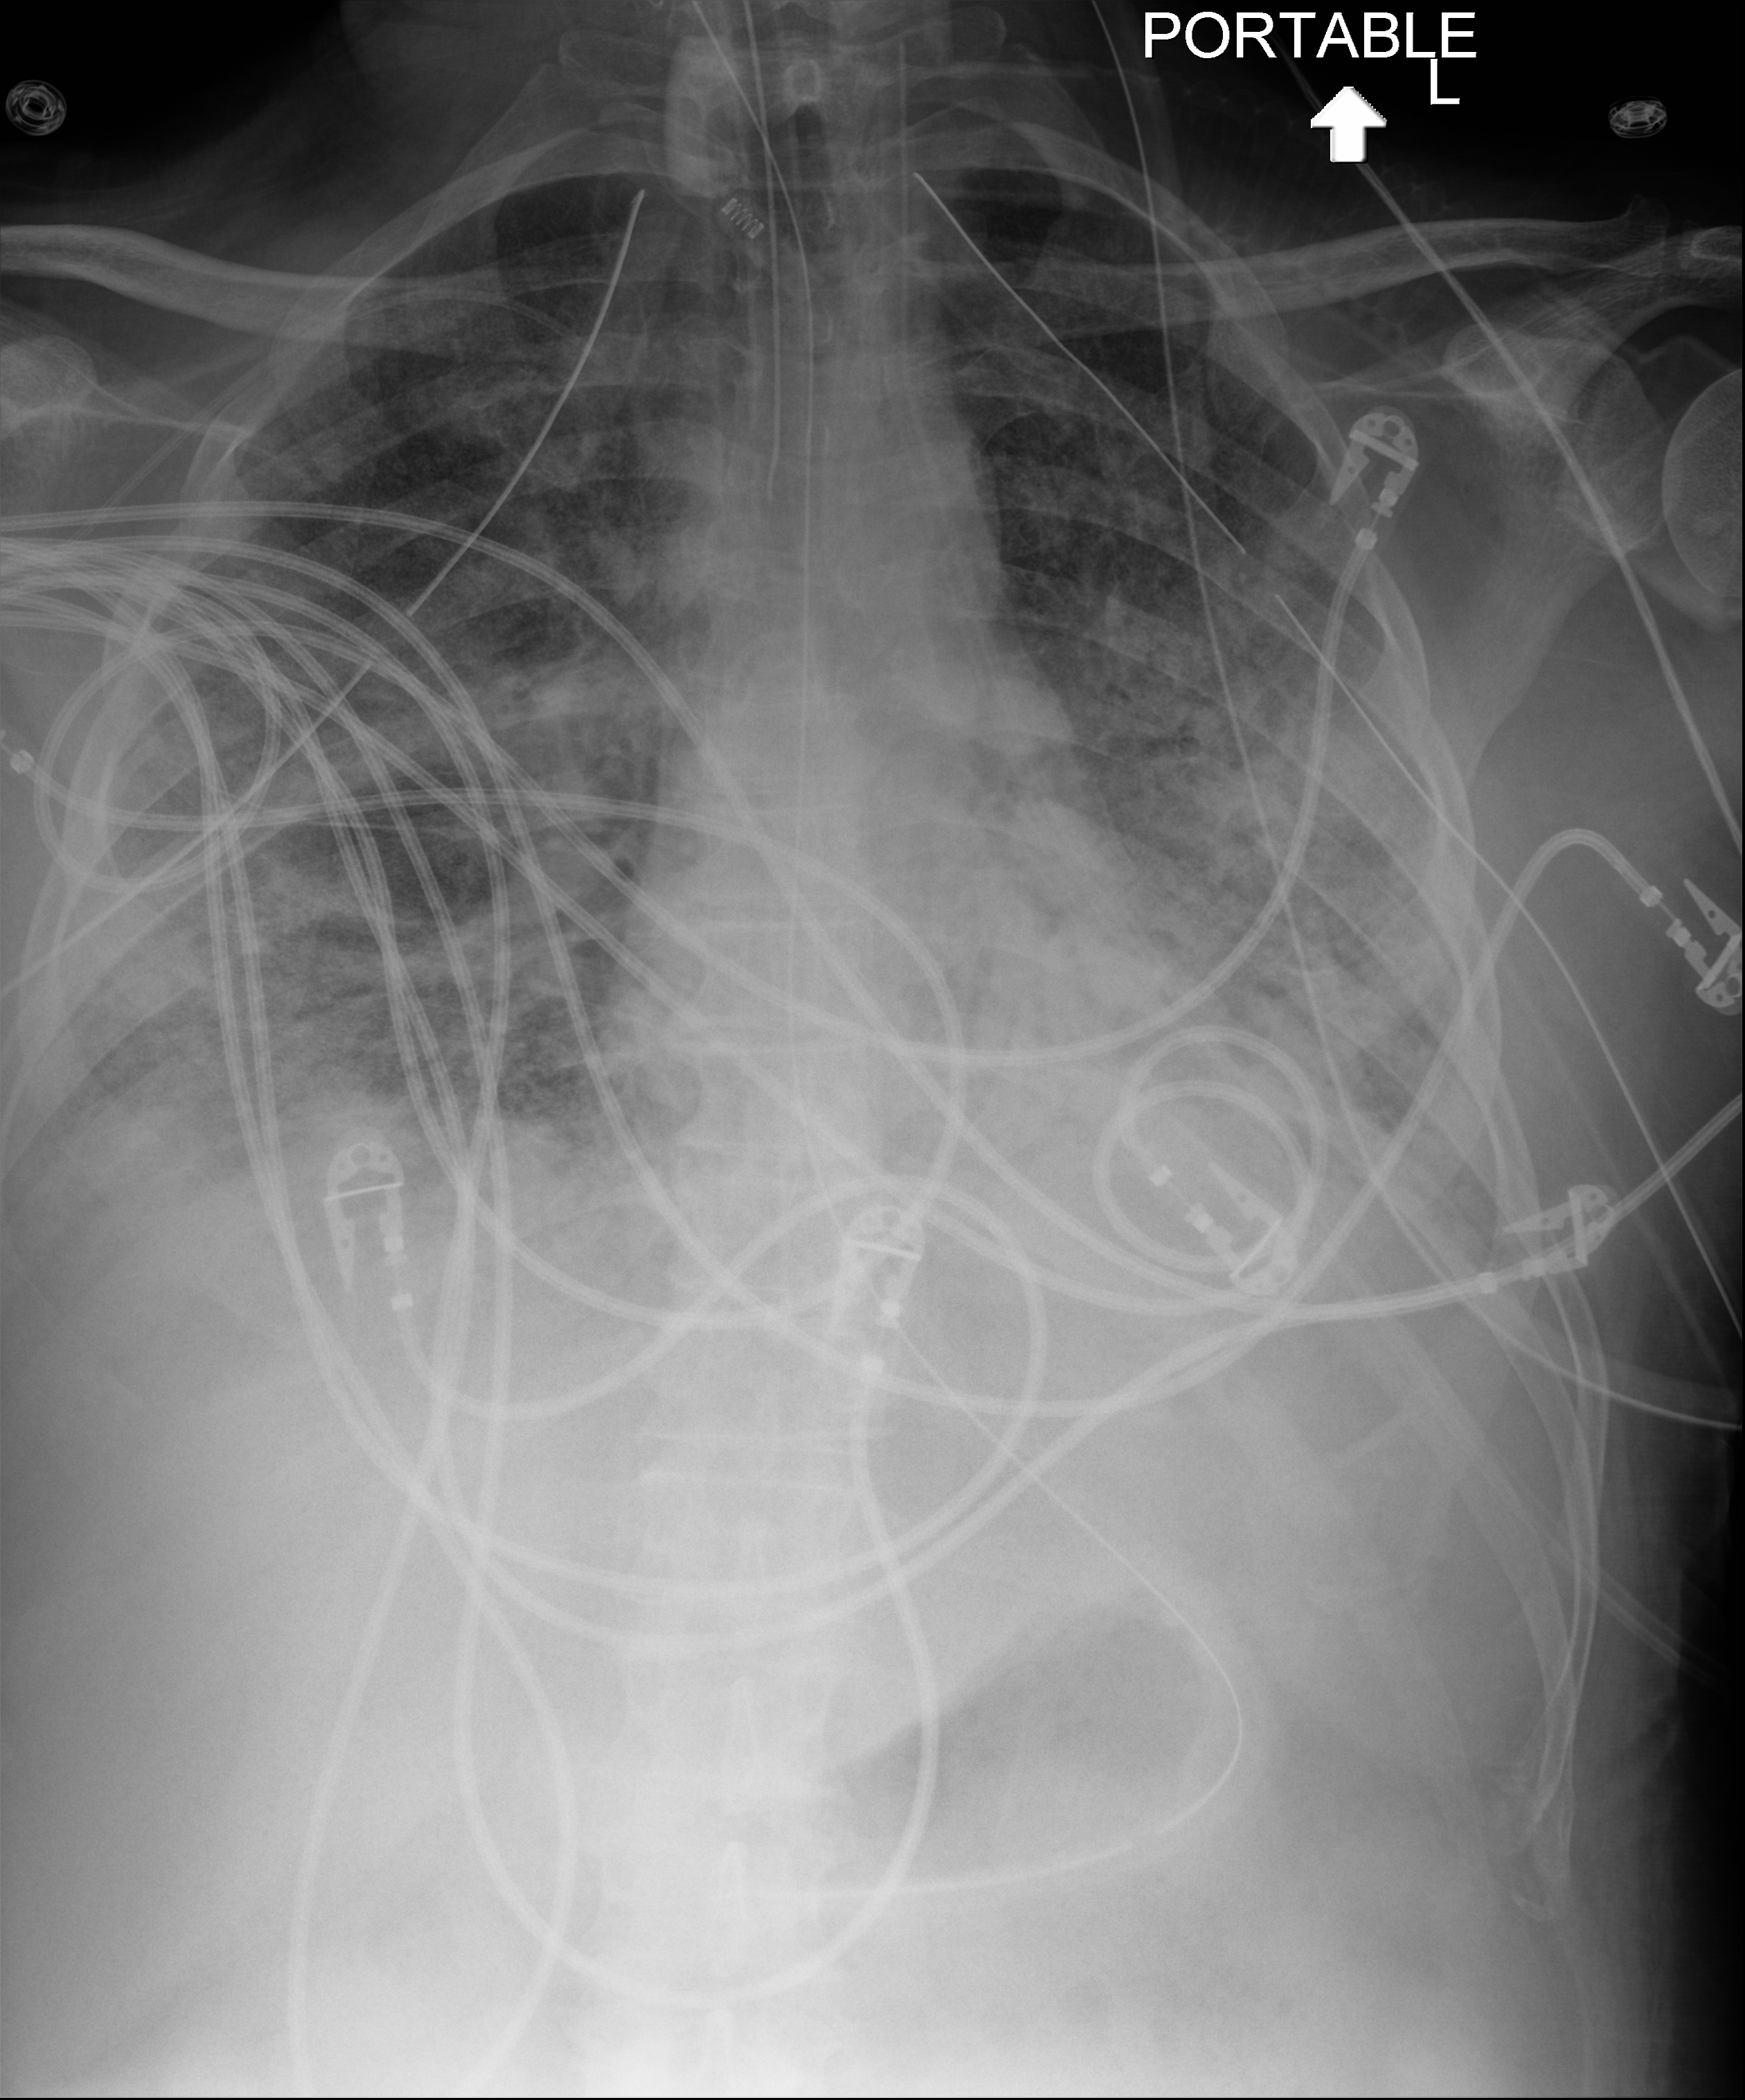
Chest X-ray (portable), anteroposterior (AP) projection. Male patient hospitalised with COVID-19, age 18–59 years.
Hospital-stay facts (about this admission, not read from this image; timing relative to this image not recorded): smoking status (admission record): never; admitted to intensive care during this hospital stay: yes.